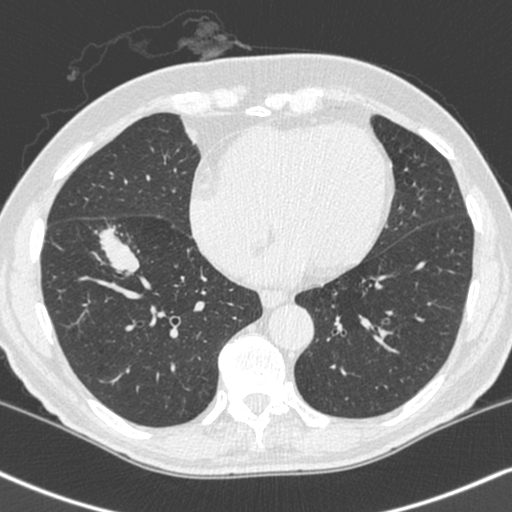
Low-dose screening chest CT, axial slice, first (baseline) screen, lung window (W 1500 / L -600 HU), slice 150 of 248 in the series. Male, age 68 years at enrolment. Current smoker at enrolment.
- Lesion marked by an expert reader, bounding box [x1, y1, x2, y2] px = [83, 215, 158, 285].
- Reader record for this screening exam (exam-level; its link to the box is not recorded): non-calcified nodule or mass ≥4 mm, right lower lobe, 34 × 17 mm, smooth margins, soft tissue attenuation.